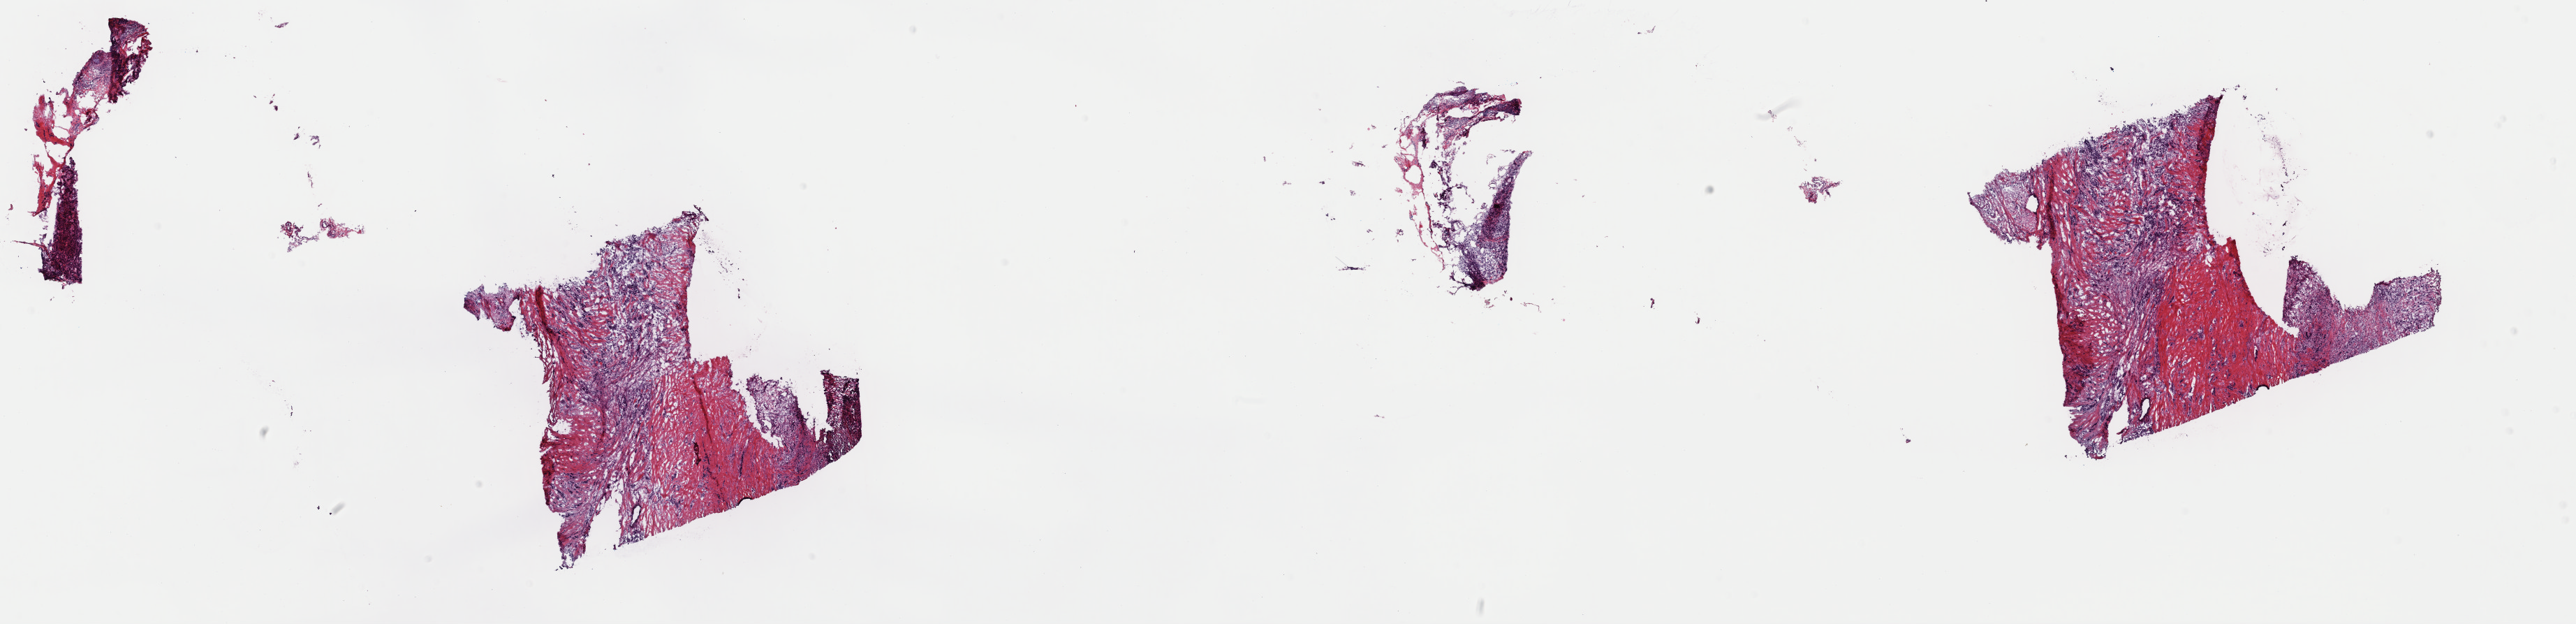
Digitized Hematoxylin and eosin (H&E) stained tissue section (whole slide), a low-resolution overview of the entire scanned area, about 29.1 x 7.1 mm (slide scanned at 40x), frozen section from the top of the tissue portion, breast, primary tumour sample. Female, age 65 years at initial diagnosis. Composition of this section per pathologist review: tumour cells 90%, tumour nuclei 75%, normal cells 10%, stromal cells 0%, necrosis 0%. Inflammatory infiltration, as recorded: lymphocyte infiltration 0%, monocyte infiltration 0%, neutrophil infiltration 0%.
* lymph nodes positive (case pathology): 0 of 3 examined
* AJCC pathologic stage: IIA
* diagnosis: Lobular carcinoma, NOS
* laterality: right